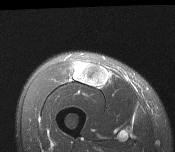
MRI of an extremity soft-tissue mass, one axial slice; position 52 of 116 along the scan axis; T2-weighted fat-saturated; MR volume resampled by the dataset authors to the PET/CT grid (not the native acquisition matrix); 3.27 mm slice thickness; 175 × 152 image matrix, field of view 171 × 148 mm. Male patient. From the clinical record (not read from this slice): histological type: pleiomorphic leiomyosarcoma; grade: intermediate; site of the primary tumour: right thigh.
Outlined on this slice (expert contour drawn on MRI and transferred to this co-registered scan by the dataset authors):
- gross tumour volume including surrounding oedema: bounding box (x1, y1, x2, y2) in pixels: (74, 63, 109, 89)